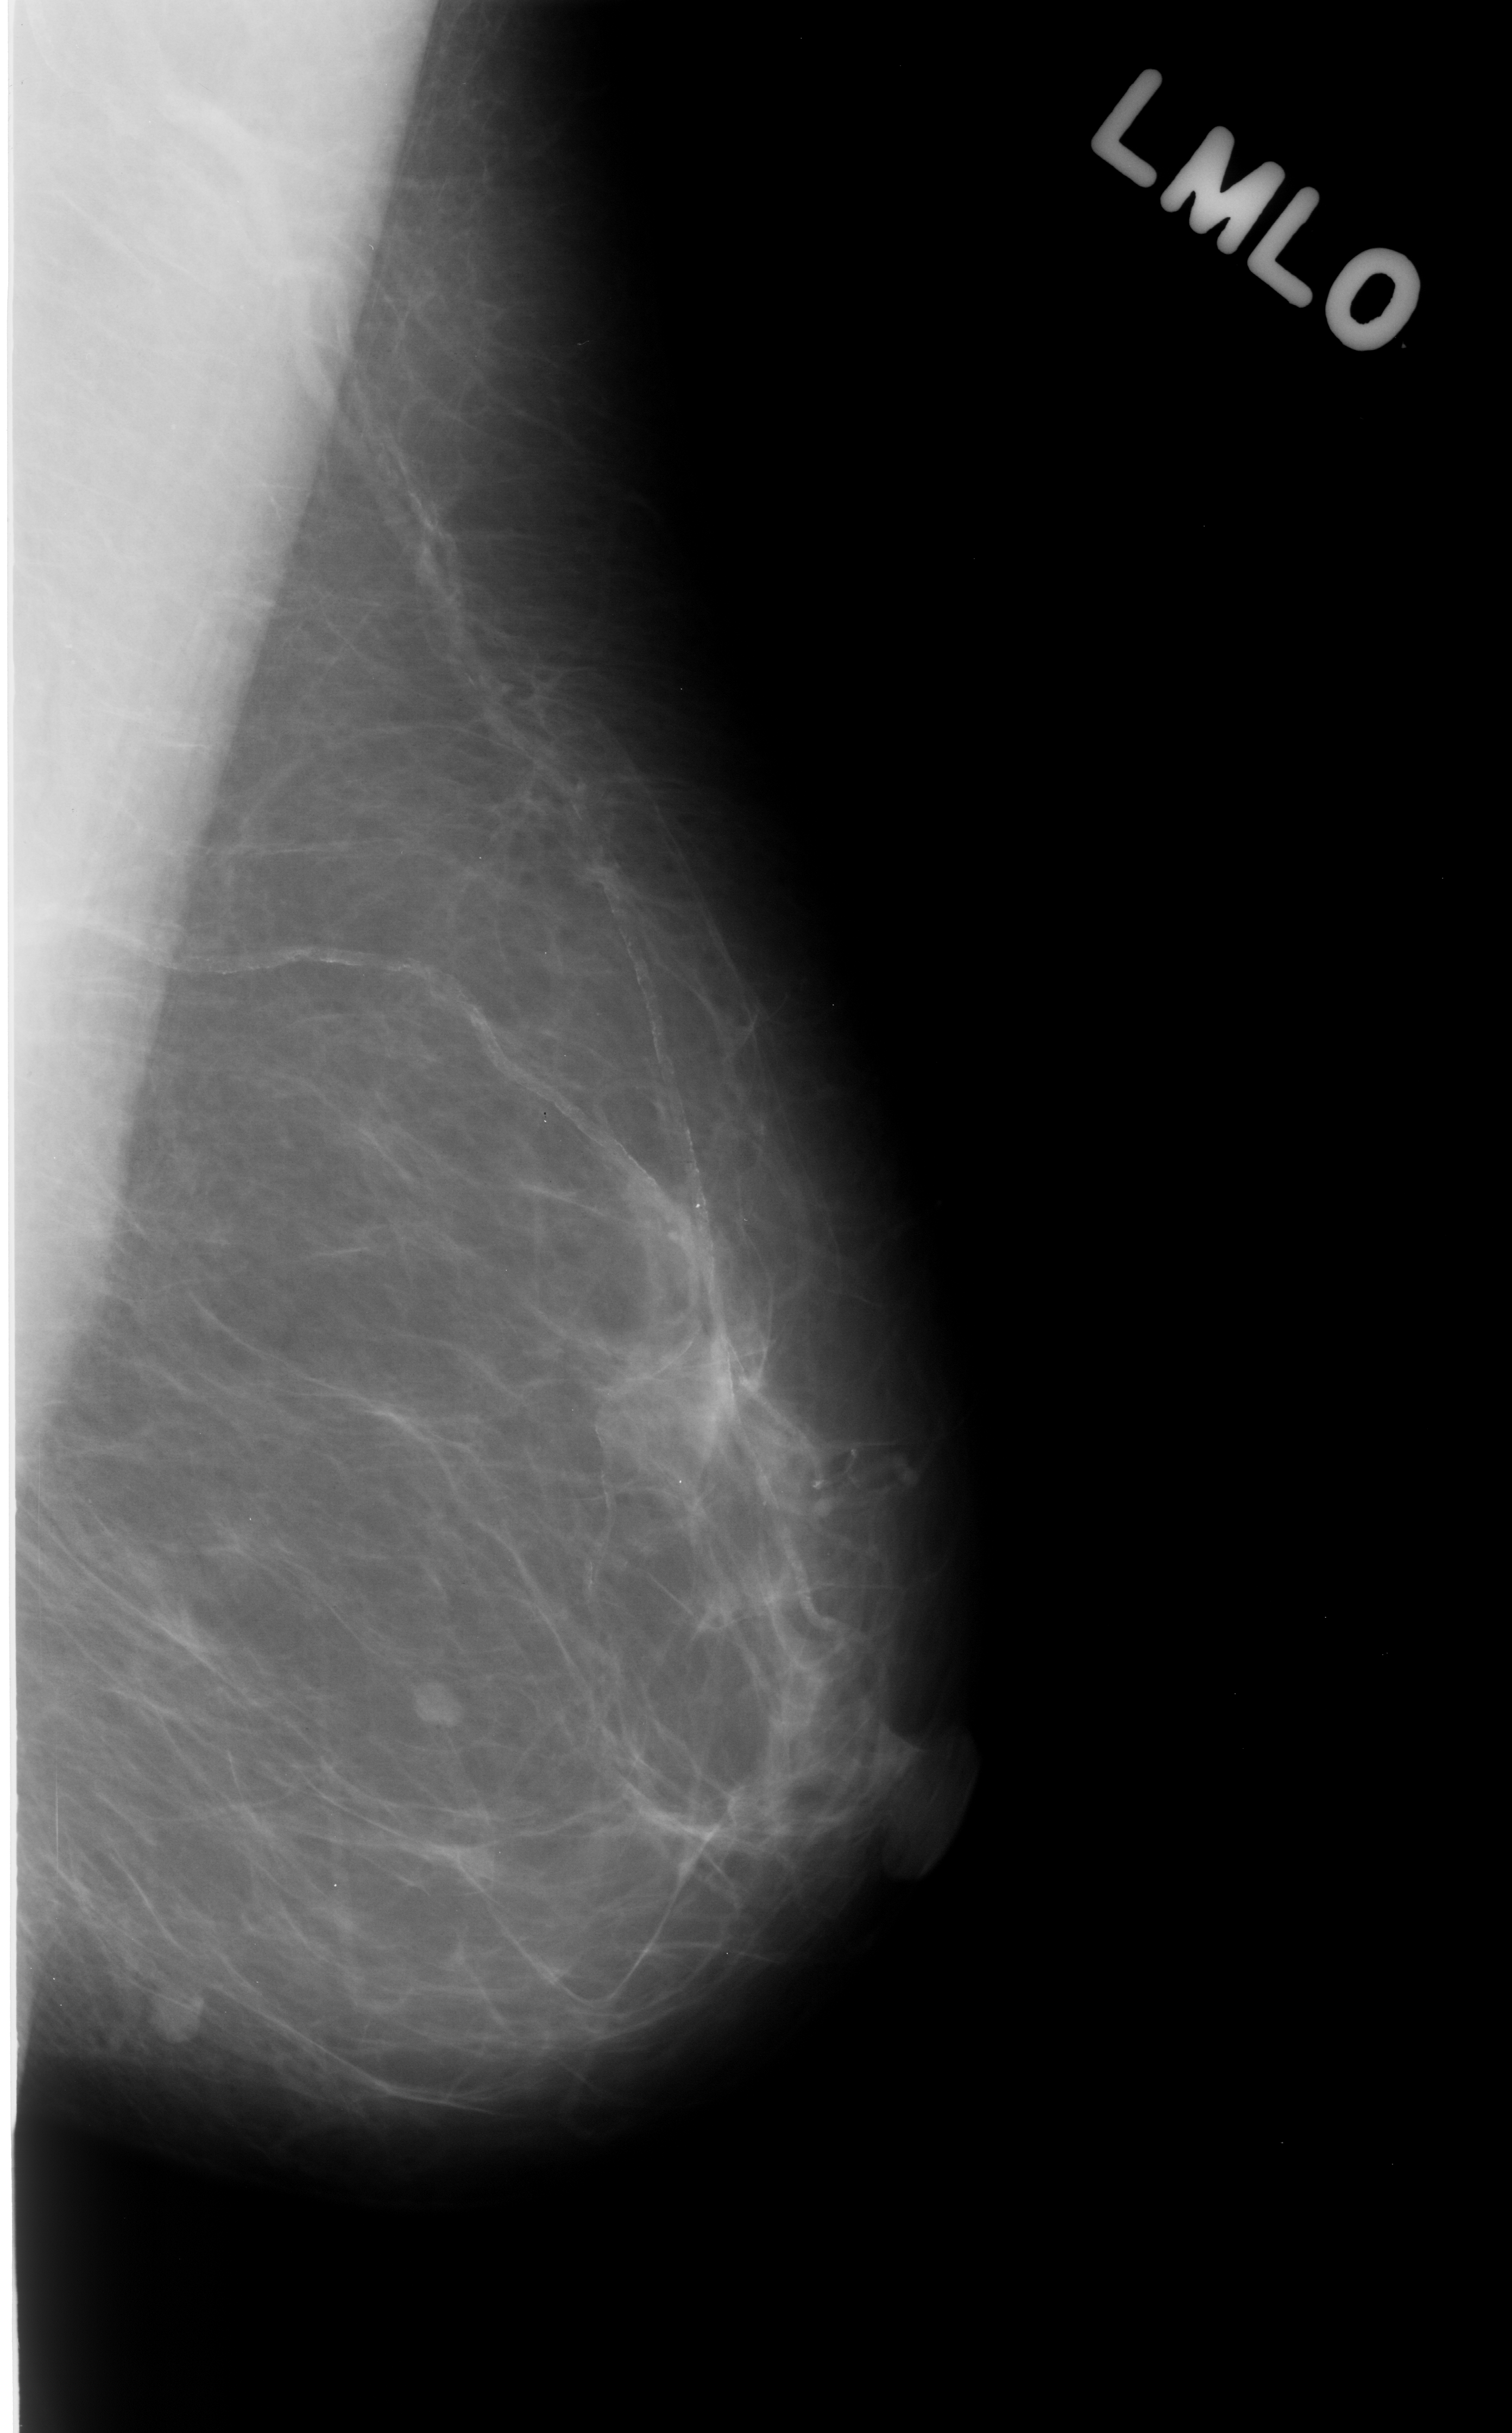
Digitized screen-film mammogram, left breast, MLO view, breast composition: almost entirely fatty (BI-RADS density category 1 of 4).
Radiologist-marked abnormalities on this image: mass, shape lobulated, margins circumscribed; BI-RADS assessment category 3; subtlety rating 5 on a 1 (subtle) to 5 (obvious) scale; pathology (as recorded): benign.